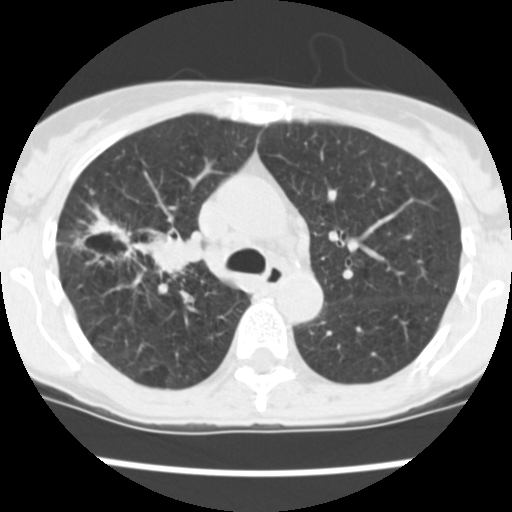
Axial slice from a low-dose chest CT screening exam, first (baseline) screen, lung window (W 1500 / L -600 HU), standard (soft-tissue) reconstruction kernel (STANDARD), slice 166 of 252 in the series, 512 × 512 image matrix. Female participant, aged 60 years at enrolment.
Lesion marked by an expert reader, bounding box [x1, y1, x2, y2] px = [82, 216, 191, 283]. The screening reader recorded 3 non-calcified nodules or masses ≥4 mm on this exam (right upper lobe, right upper lobe, right lower lobe); which of them this box marks is not recorded. Lung cancer was diagnosed 19 days after this screen: non-small cell carcinoma, right upper lobe, stage IV (AJCC 6th edition), 26 mm at pathology.